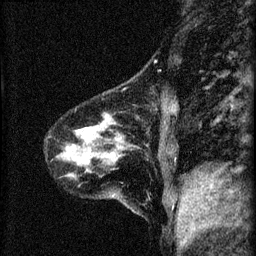
Breast MRI (dynamic contrast-enhanced), one sagittal slice. Slice 11 of 60 in the series (ordered by position). Dynamic contrast-enhanced series, image 2 of 4 at this slice position (ordered by acquisition). 1.5 T. TE 4.2 ms, TR 8.2 ms. 2 mm slice thickness. 256 × 256 image matrix. Patient: female, 41 years.
Annotated regions visible in this slice (semi-automatically segmented with operator editing):
- analysis volume of interest (the breast-tissue region the enhancement analysis was run in; not a lesion): bounding box [x1, y1, x2, y2] px = [57, 98, 166, 210]
- tumour enhancement mask (voxels above the 70 % enhancement threshold inside the analysis volume of interest): [88, 131, 94, 133]